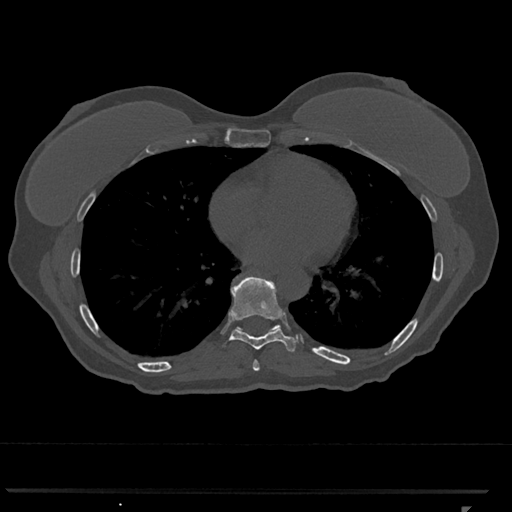
CT including the spine, one axial slice. Position 659 of 793 along the scan axis. 120 kVp. Bone window (W 1800 / L 400 HU). 0.5 mm slice thickness. 512 × 512 image matrix, field of view 380 × 380 mm. Patient: female, 62 years. Case-level facts recorded for this patient, not image findings: primary cancer: renal.
Annotated regions visible in this slice (semi-automatically segmented with operator editing):
- T7 vertebra: bounding box <253,360,260,371> (left, top, right, bottom; pixels)
- T8 vertebra: <229,277,299,352>
- T9 vertebra: <234,277,281,331>